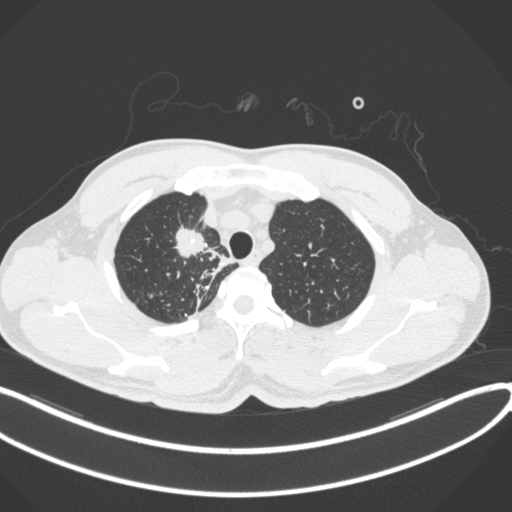
Chest CT, one axial slice; position 316 of 391 along the scan axis; 120 kVp; lung window (W 1500 / L -600 HU); 512 × 512 image matrix. Male patient, age 48 years. Case-level facts recorded for this patient, not image findings: clinical TNM (as recorded): T1c N1 M1.
Structures marked on this image (rectangle marked by the reading radiologist):
- lung tumour (recorded histology: adenocarcinoma): bounding box (x1, y1, x2, y2) in pixels: (170, 222, 209, 261)